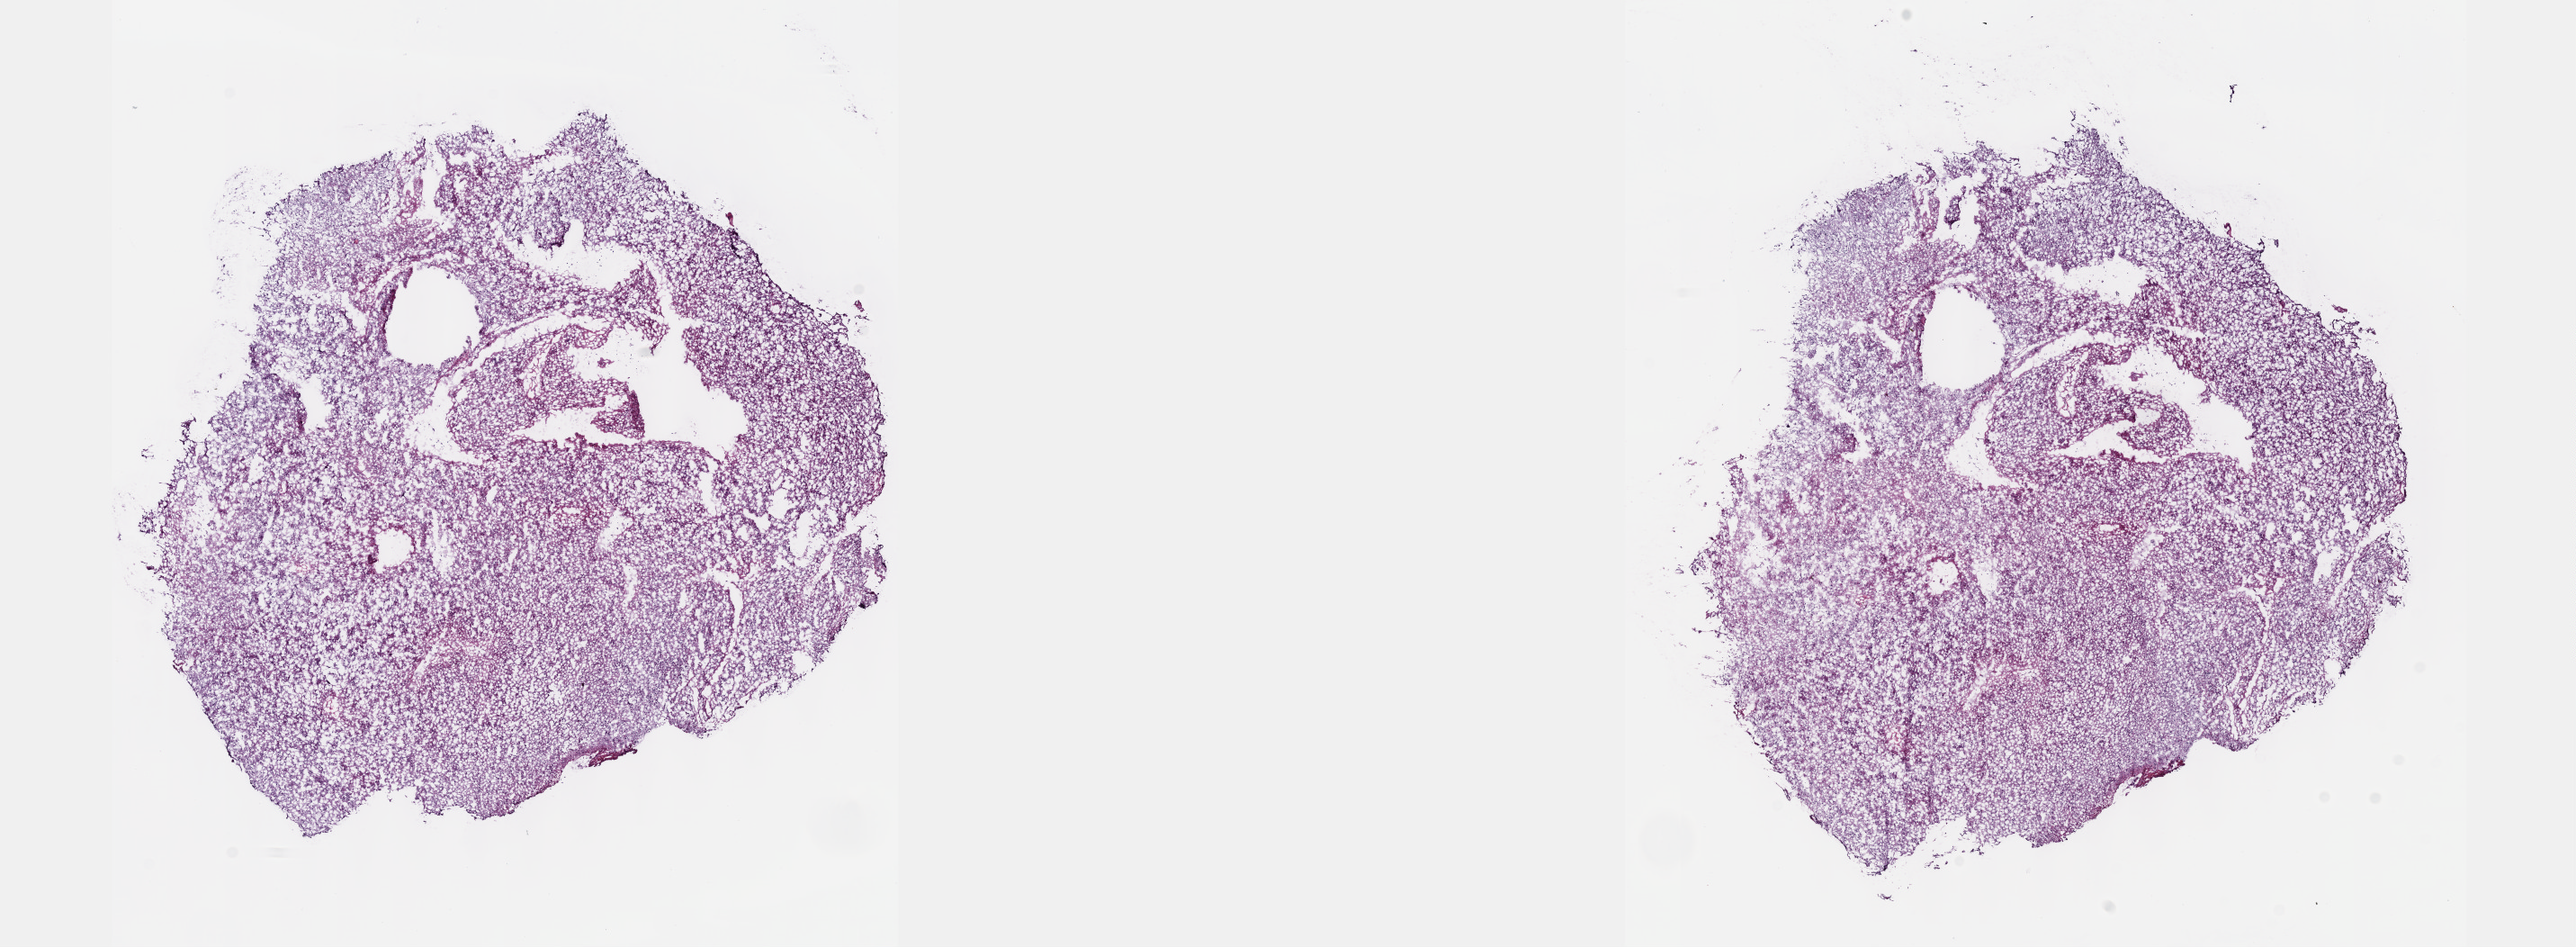
H&E whole-slide image, shown as a low-resolution overview of the whole scanned area (about 23.1 x 8.5 mm, from a 40x scan). Frozen section. Brain, primary tumour sample. Patient: male, age at initial diagnosis 35 years. Histologic grade: G2 (moderately differentiated). Composition of this section per pathologist review: tumour cells 45%, tumour nuclei 85%, normal cells 10%, stromal cells 45%, necrosis 0%. Infiltration values recorded for this section: lymphocyte infiltration 0%, monocyte infiltration 0%, neutrophil infiltration 0%.
• diagnosis: Astrocytoma, NOS (cerebrum)